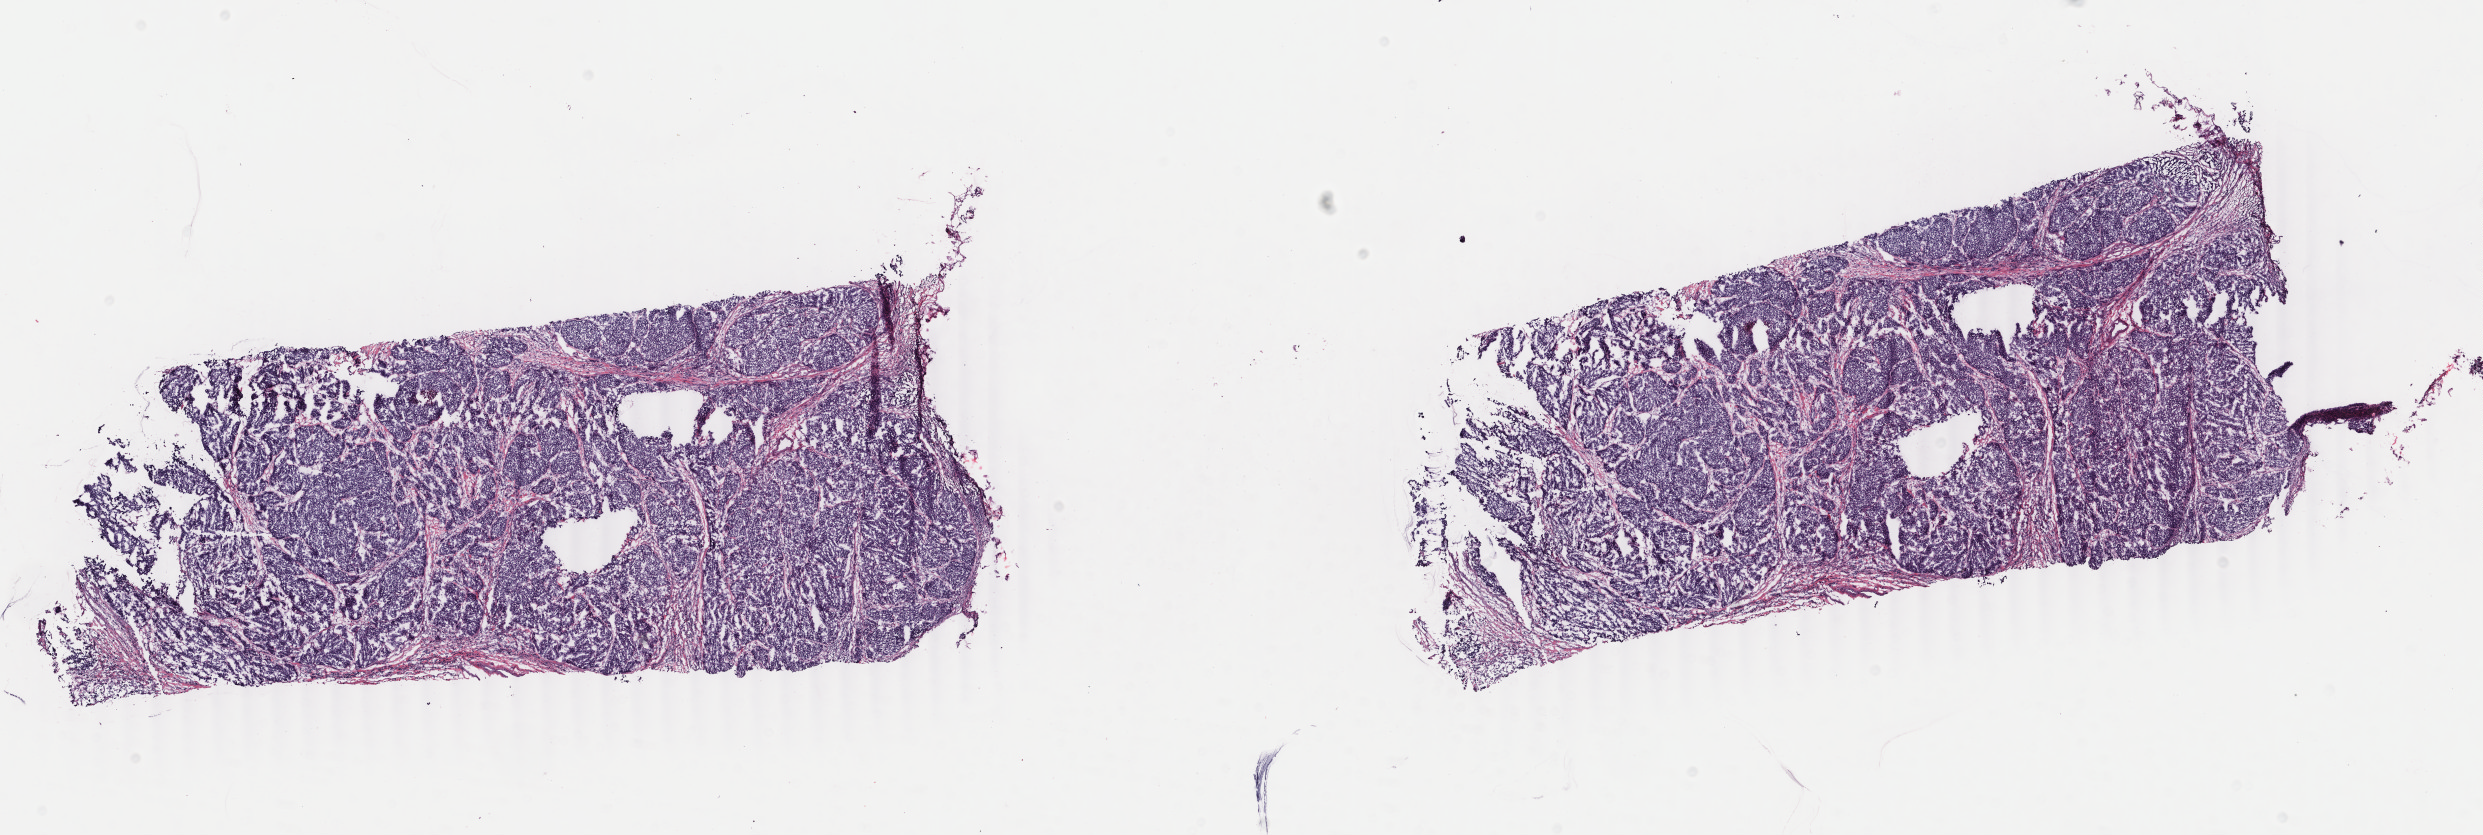
H&E-stained whole-slide image, shown as a low-resolution overview of the whole scanned area (about 19.8 x 6.6 mm), frozen section from the top of the tissue portion, breast, primary tumour sample. Patient: female, age at initial diagnosis 66 years. Slide review estimates, as recorded: tumour cells 90%, tumour nuclei 90%, normal cells 0%, stromal cells 9%, necrosis 1%. Inflammatory infiltration, as recorded: lymphocyte infiltration 2%, monocyte infiltration 0%, neutrophil infiltration 0%.
TNM: T2 N0 M0. Laterality: left. Diagnosis: Infiltrating duct carcinoma, NOS. AJCC pathologic stage: IIA (6th edition). Lymph nodes positive (case pathology): 0 of 3 examined.